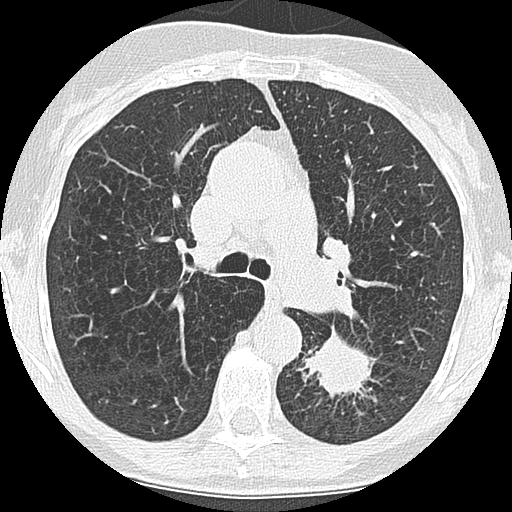
Low-dose screening chest CT, one axial slice. Slice 114 of 171 in the series (ordered by position). 120 kVp. Lung window (W 1500 / L -600 HU). 2.5 mm slice thickness. 512 × 512 image matrix, field of view 280 × 280 mm.
Outlined on this slice (outlined manually by an expert reader):
- lesion 1 (tumor, lower lobe of left lung): bounding box (x1, y1, x2, y2) in pixels: (305, 336, 371, 395)